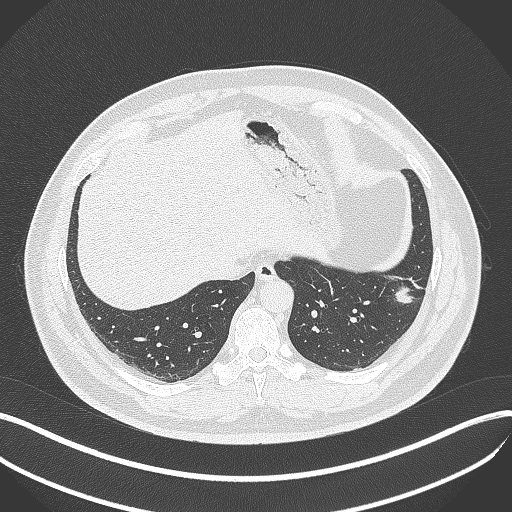
Chest CT, one axial slice. Position 109 of 429 along the scan axis. 120 kVp. Lung window (W 1500 / L -600 HU). 512 × 512 image matrix, field of view 400 × 400 mm. Male patient, age 39 years. From the clinical record (not read from this slice): clinical TNM (as recorded): T2a N0 M0.
Outlined on this slice (rectangle marked by the reading radiologist):
- lung tumour (recorded histology: adenocarcinoma): bounding box <391,282,419,307> (left, top, right, bottom; pixels)